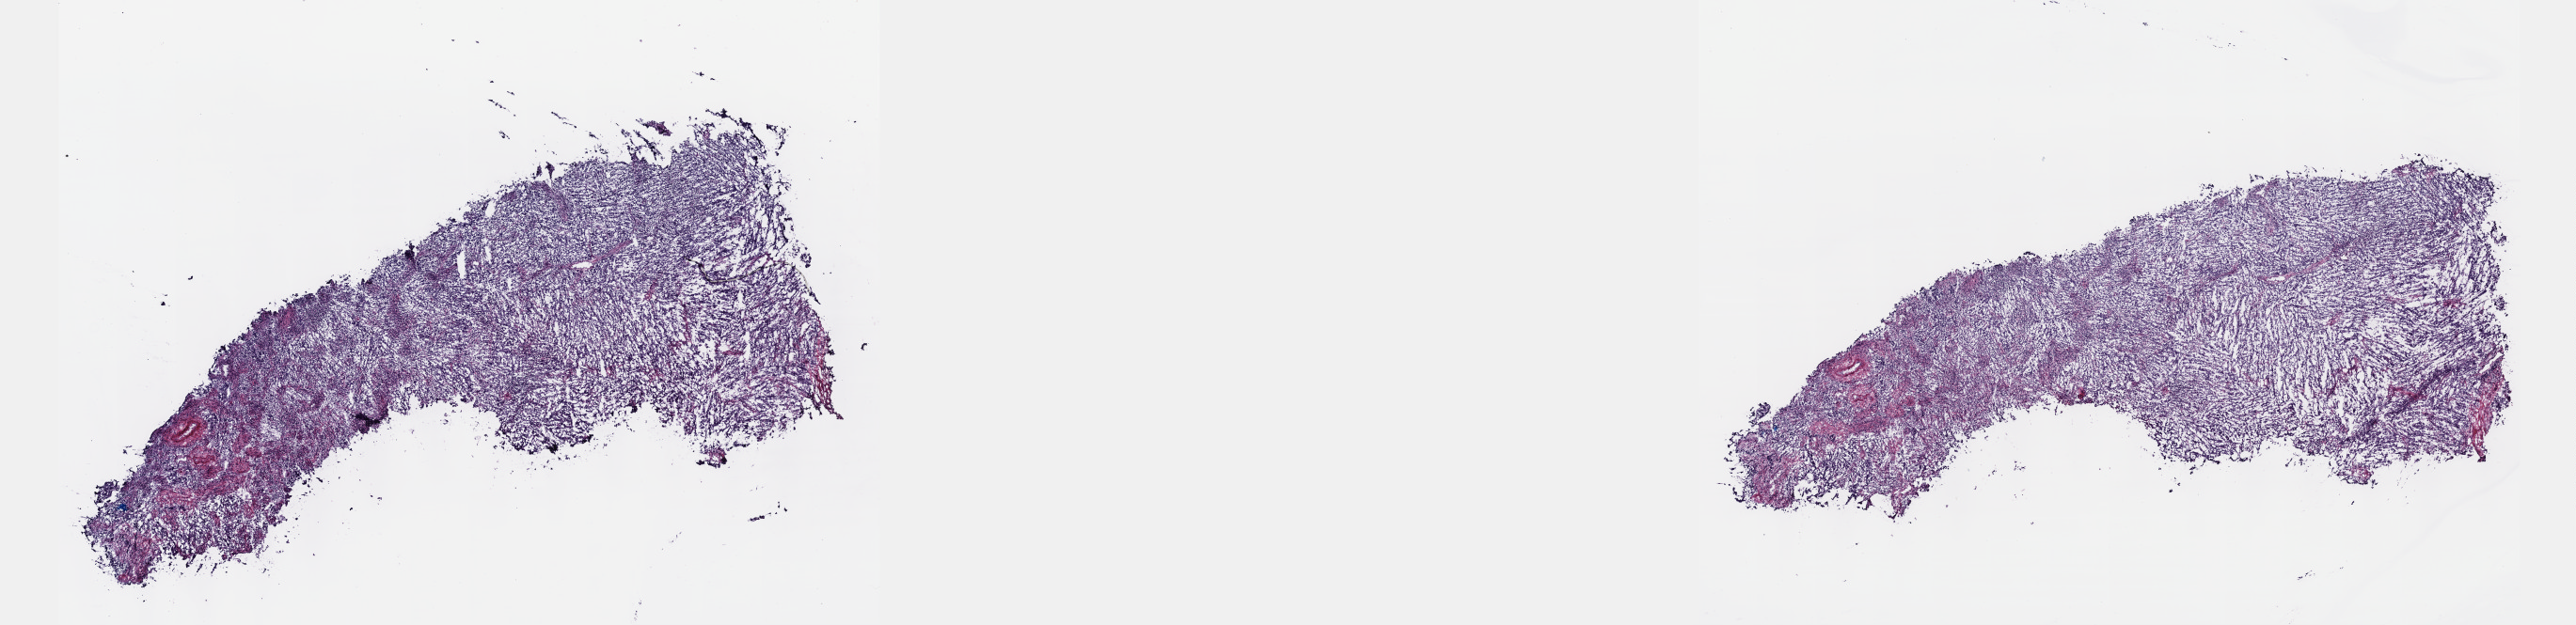
Whole-slide histology image, H&E-stained — whole scanned area (about 22.1 x 5.4 mm) shown as a low-resolution overview. Frozen section. Primary tumour sample from the testis. Male, age 38 years at initial diagnosis. Composition of this section per pathologist review: tumour cells 90%, tumour nuclei 60%, normal cells 0%, stromal cells 10%, necrosis 0%. Infiltration values recorded for this section: lymphocyte infiltration 90%, monocyte infiltration 10%, neutrophil infiltration 0%.
AJCC pathologic stage: IB. Histologic diagnosis: Seminoma, NOS.